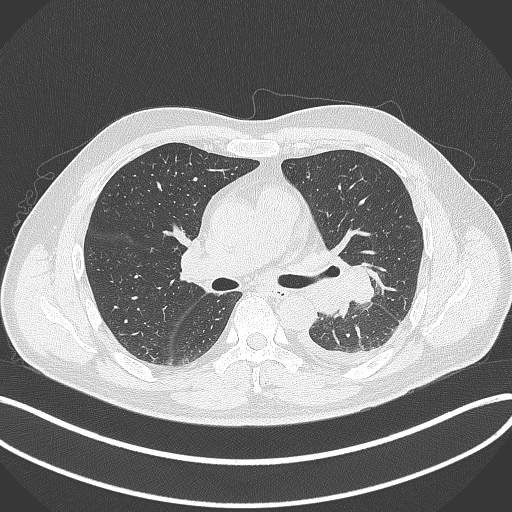
Chest CT, one axial slice. Slice 211 of 342 in the series (ordered by position). Reconstruction kernel B70f. 120 kVp. Lung window (W 1500 / L -600 HU). 1 mm slice thickness. 512 × 512 image matrix, field of view 400 × 400 mm. Male patient, age 58 years. From the clinical record (not read from this slice): clinical TNM (as recorded): T3 N1 M1b; histopathological grade: G3.
Structures marked on this image (rectangle marked by the reading radiologist):
- lung tumour (recorded histology: small cell carcinoma): bounding box (x1, y1, x2, y2) in pixels: (340, 260, 378, 307)